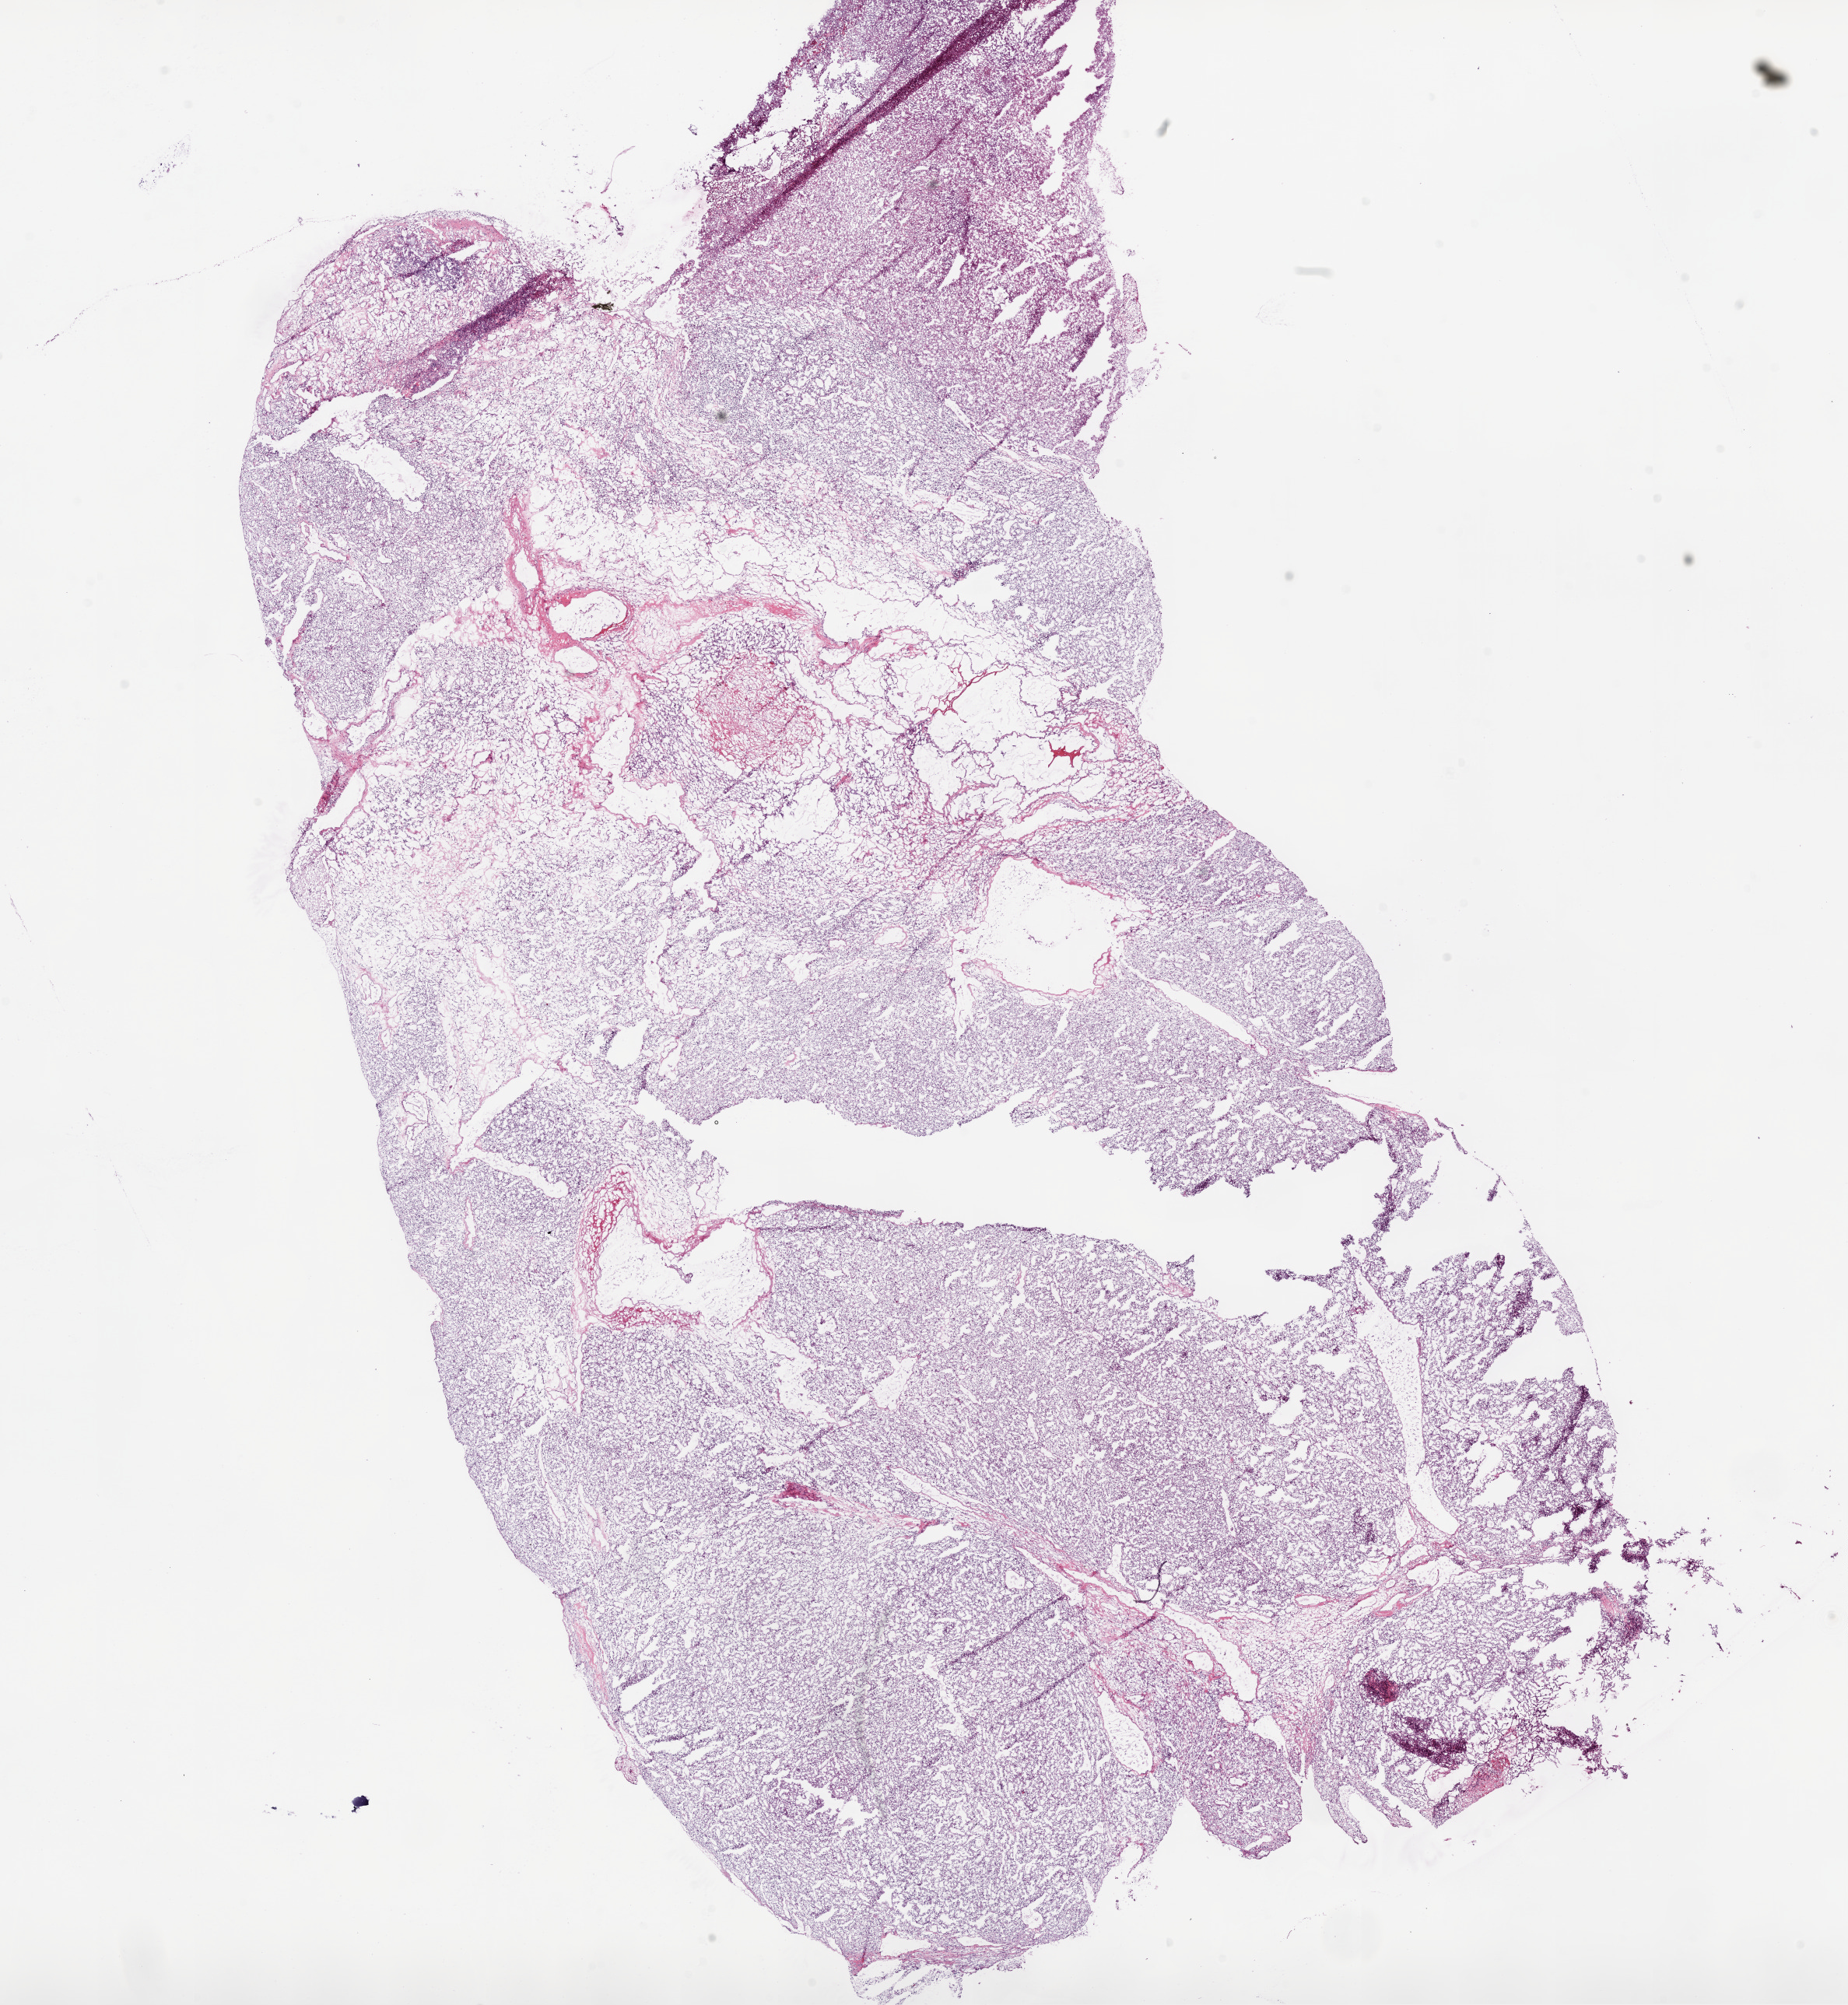
Hematoxylin and eosin (H&E) stained whole-slide image — low-resolution overview of the scanned area, about 19.1 x 20.7 mm, frozen section from the bottom of the tissue portion, primary tumour sample from the kidney. Patient: female, age at initial diagnosis 75 years. Histologic grade: G2 (moderately differentiated). Pathologist review of this section (percent, as recorded): tumour cells 90%, tumour nuclei 90%, normal cells 0%, stromal cells 10%, necrosis 0%.
- pathologic diagnosis: Clear cell adenocarcinoma, NOS
- AJCC pathologic stage: II
- lymph nodes positive (case pathology): 0 of 6 examined